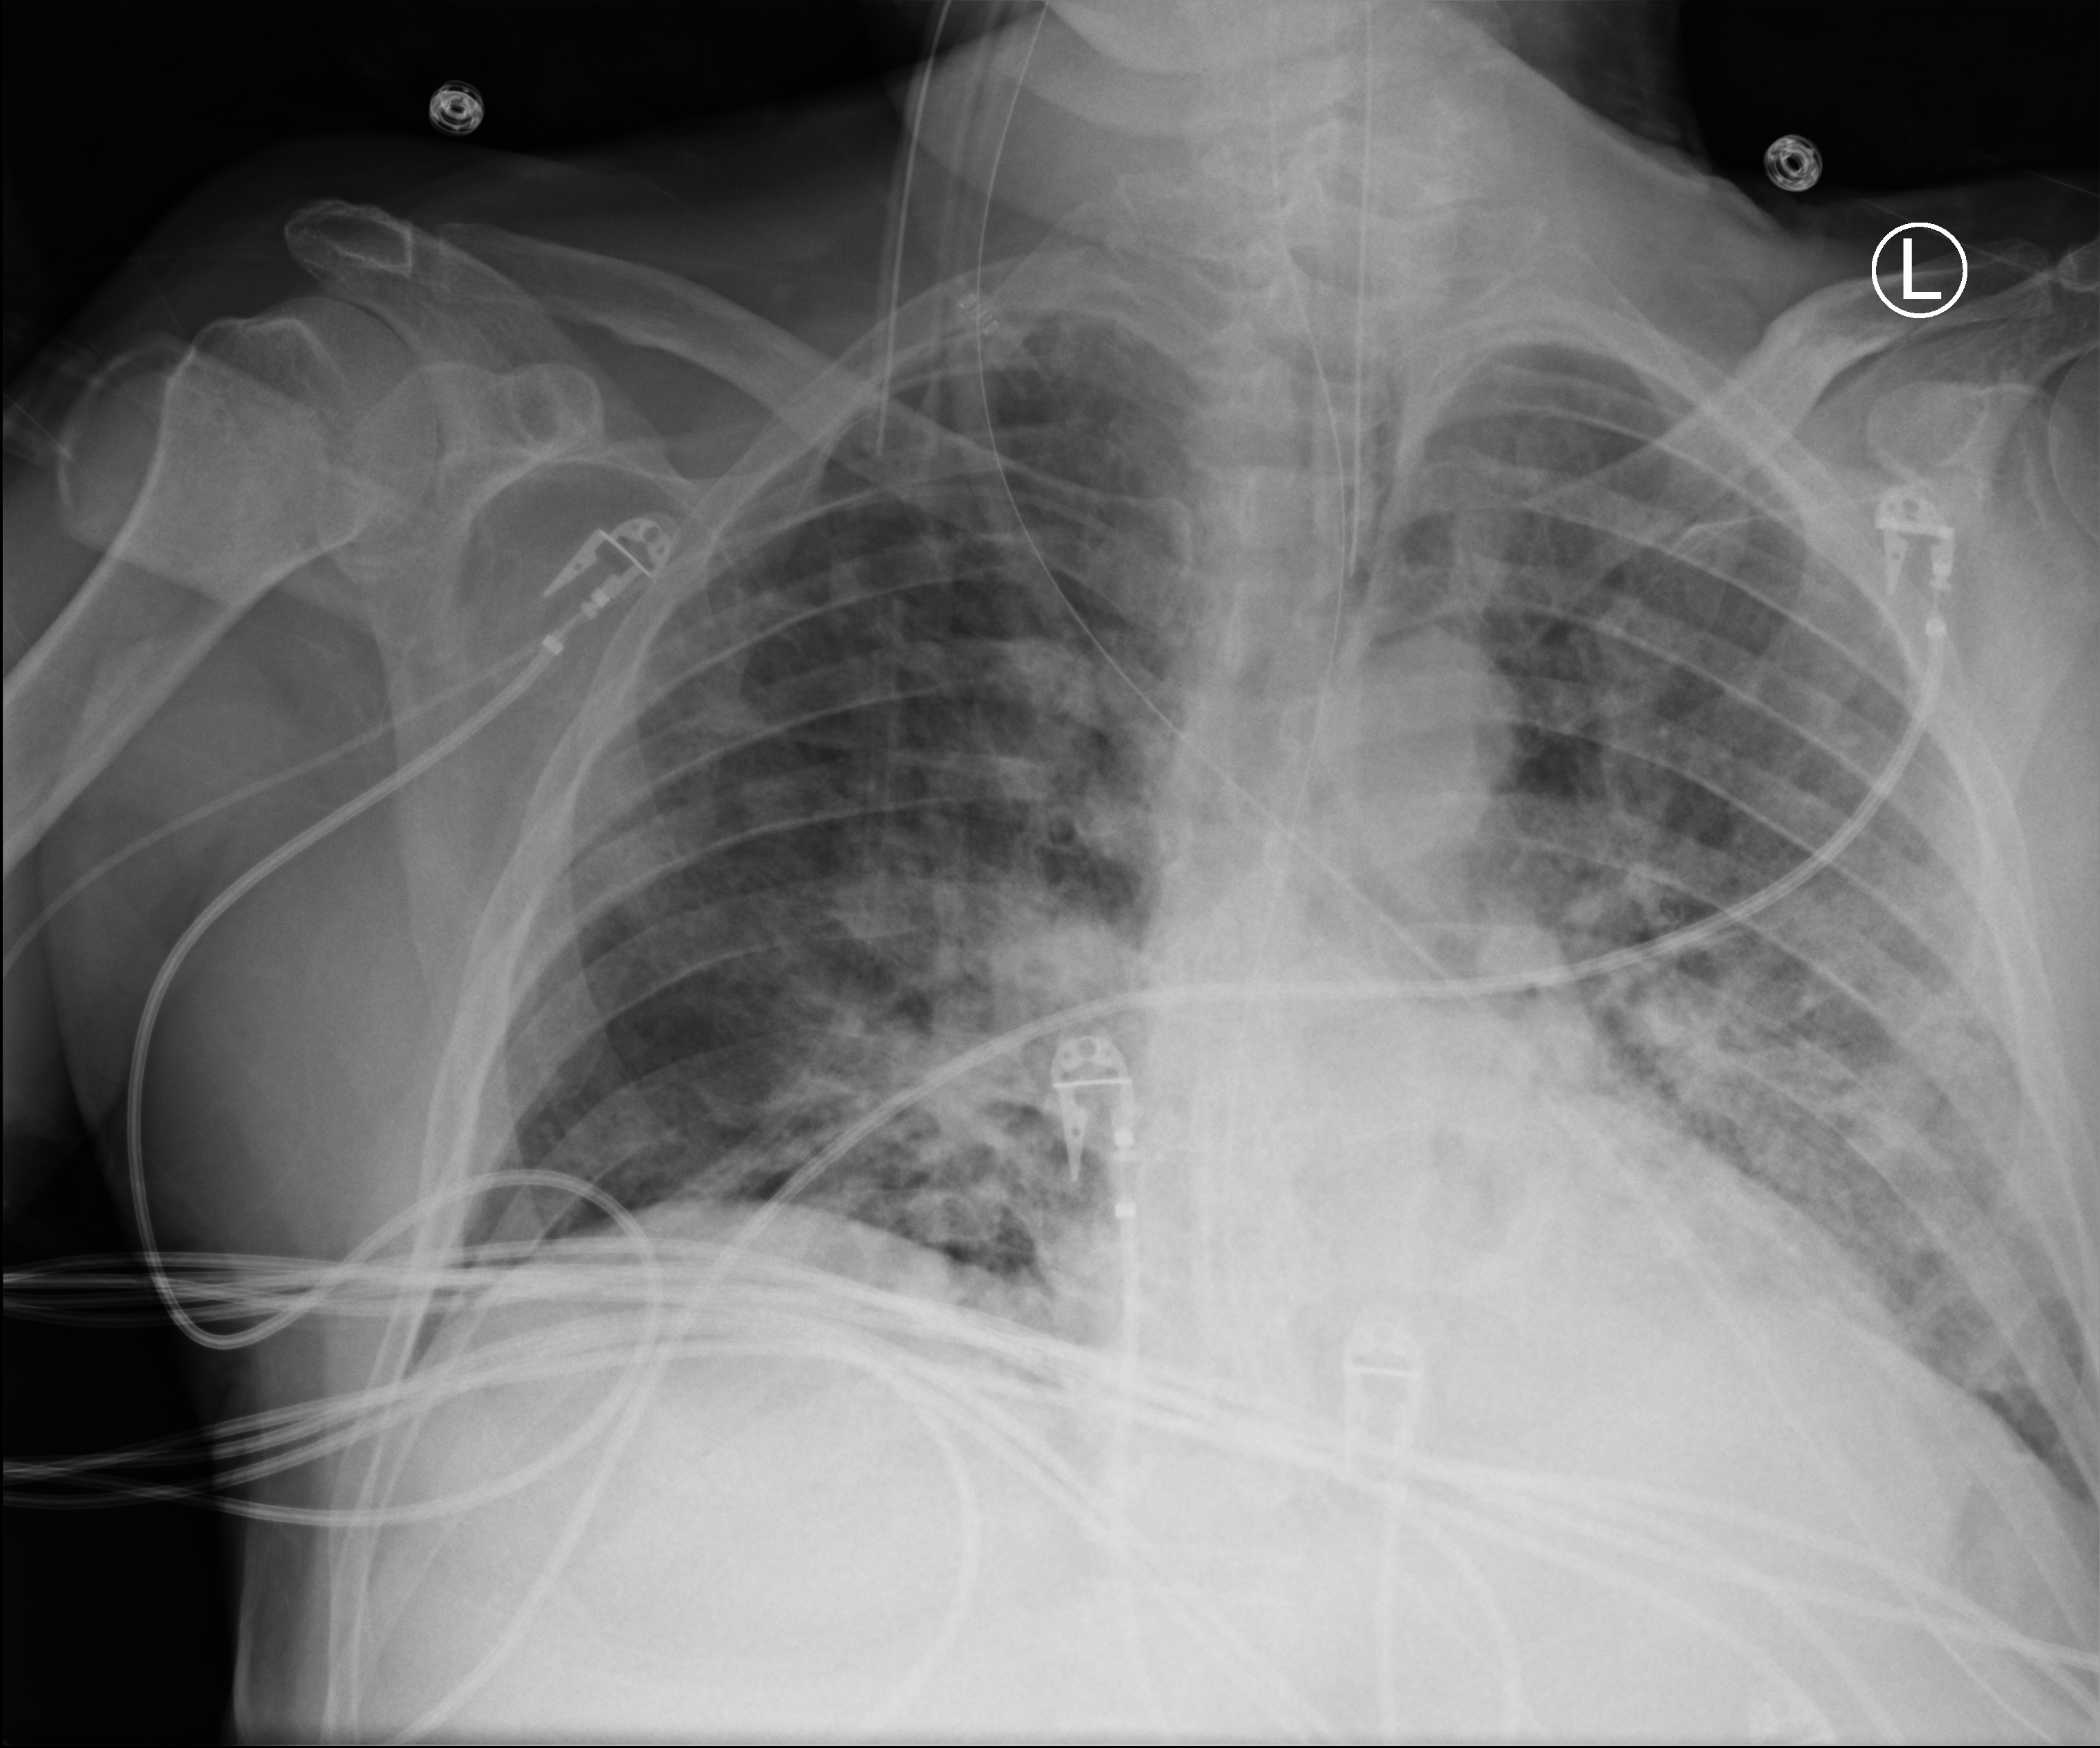
Portable chest radiograph. Male patient hospitalised with COVID-19, age 60–74 years.
Hospital-stay facts (about this admission, not read from this image; timing relative to this image not recorded): other chronic lung disease (admission record): no.